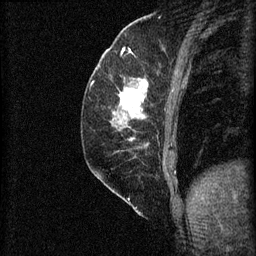
Breast MRI (dynamic contrast-enhanced), one sagittal slice. 3 images stored at this slice position (order not interpretable as contrast timing). 1.5 T. TE 4.2 ms, TR 8.2 ms. 2 mm slice thickness. 256 × 256 image matrix, field of view 180 × 180 mm. Female patient, age 59 years.
Outlined on this slice (semi-automatically segmented with operator editing):
- analysis volume of interest (the breast-tissue region the enhancement analysis was run in; not a lesion): bounding box <92,74,150,131> (left, top, right, bottom; pixels)
- tumour enhancement mask (voxels above the 70 % enhancement threshold inside the analysis volume of interest): <120,80,149,119>